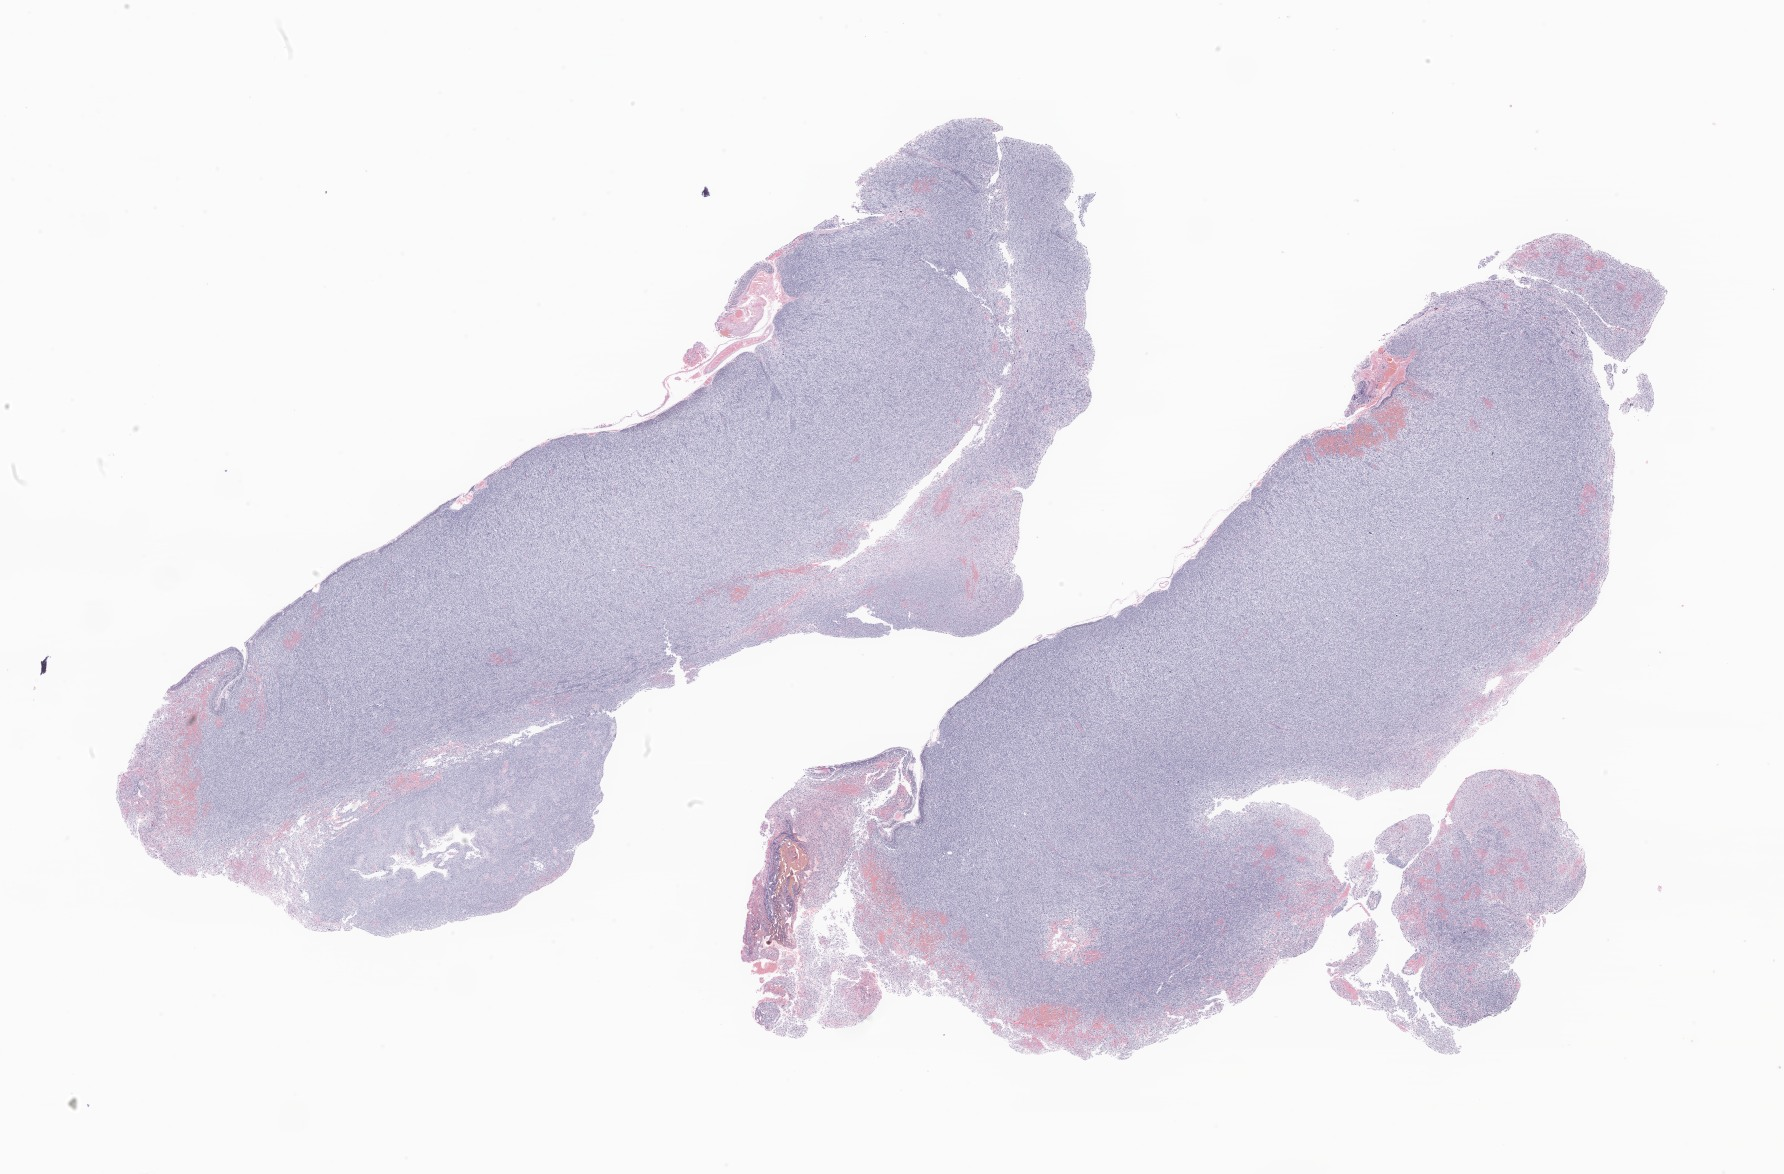
Digitized haematoxylin and eosin-stained section of tumor tissue from the frontal lobe, low-resolution overview of the scanned area, about 30.1 x 19.8 mm, FFPE section. Patient male; age 204 months (17 years).
Diagnosis: Glioma, malignant.